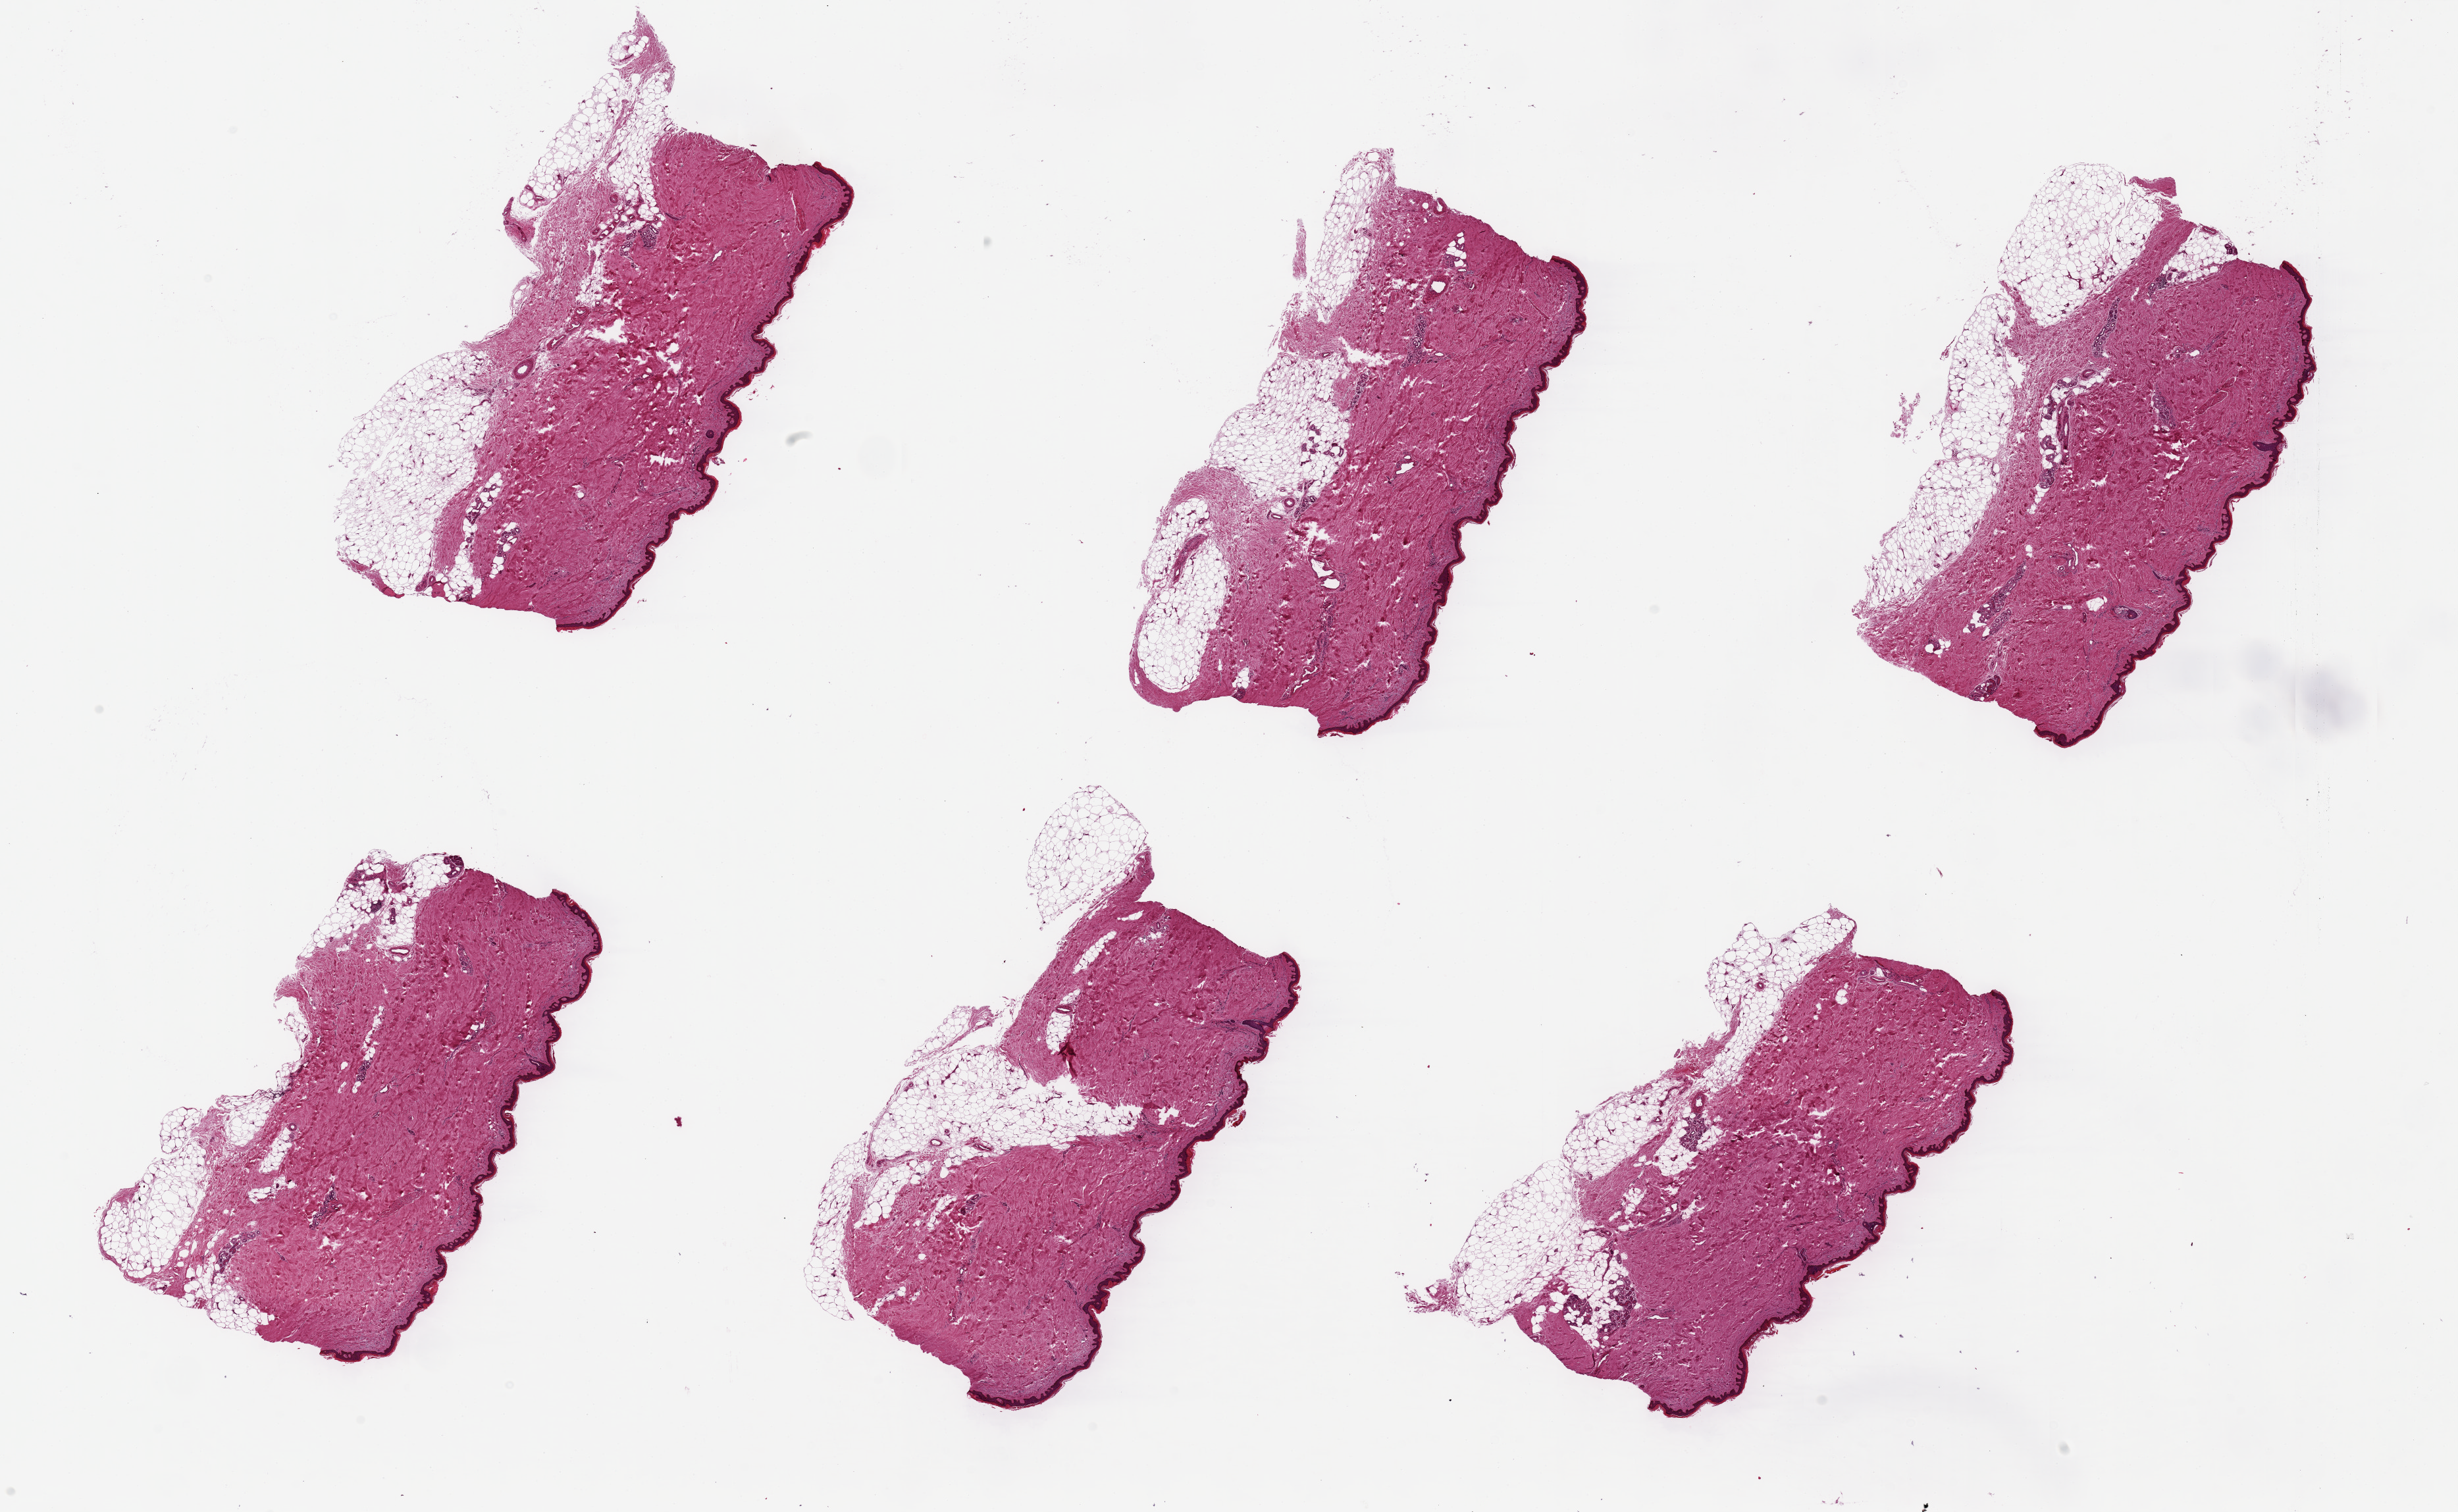
Digitized H&E-stained section, brightfield, low-resolution overview of the scanned area, about 29.5 x 18.2 mm (slide scanned at 20x). PAXgene-fixed, paraffin-embedded tissue. Sampled site (target tissue): skin of lower leg. Donor tissue sample. Male donor.
Pathologist's review note for this sample: 6 pieces, up to 8x4.5mm; too much subcutaneous adipose (up to 1.5 mm).